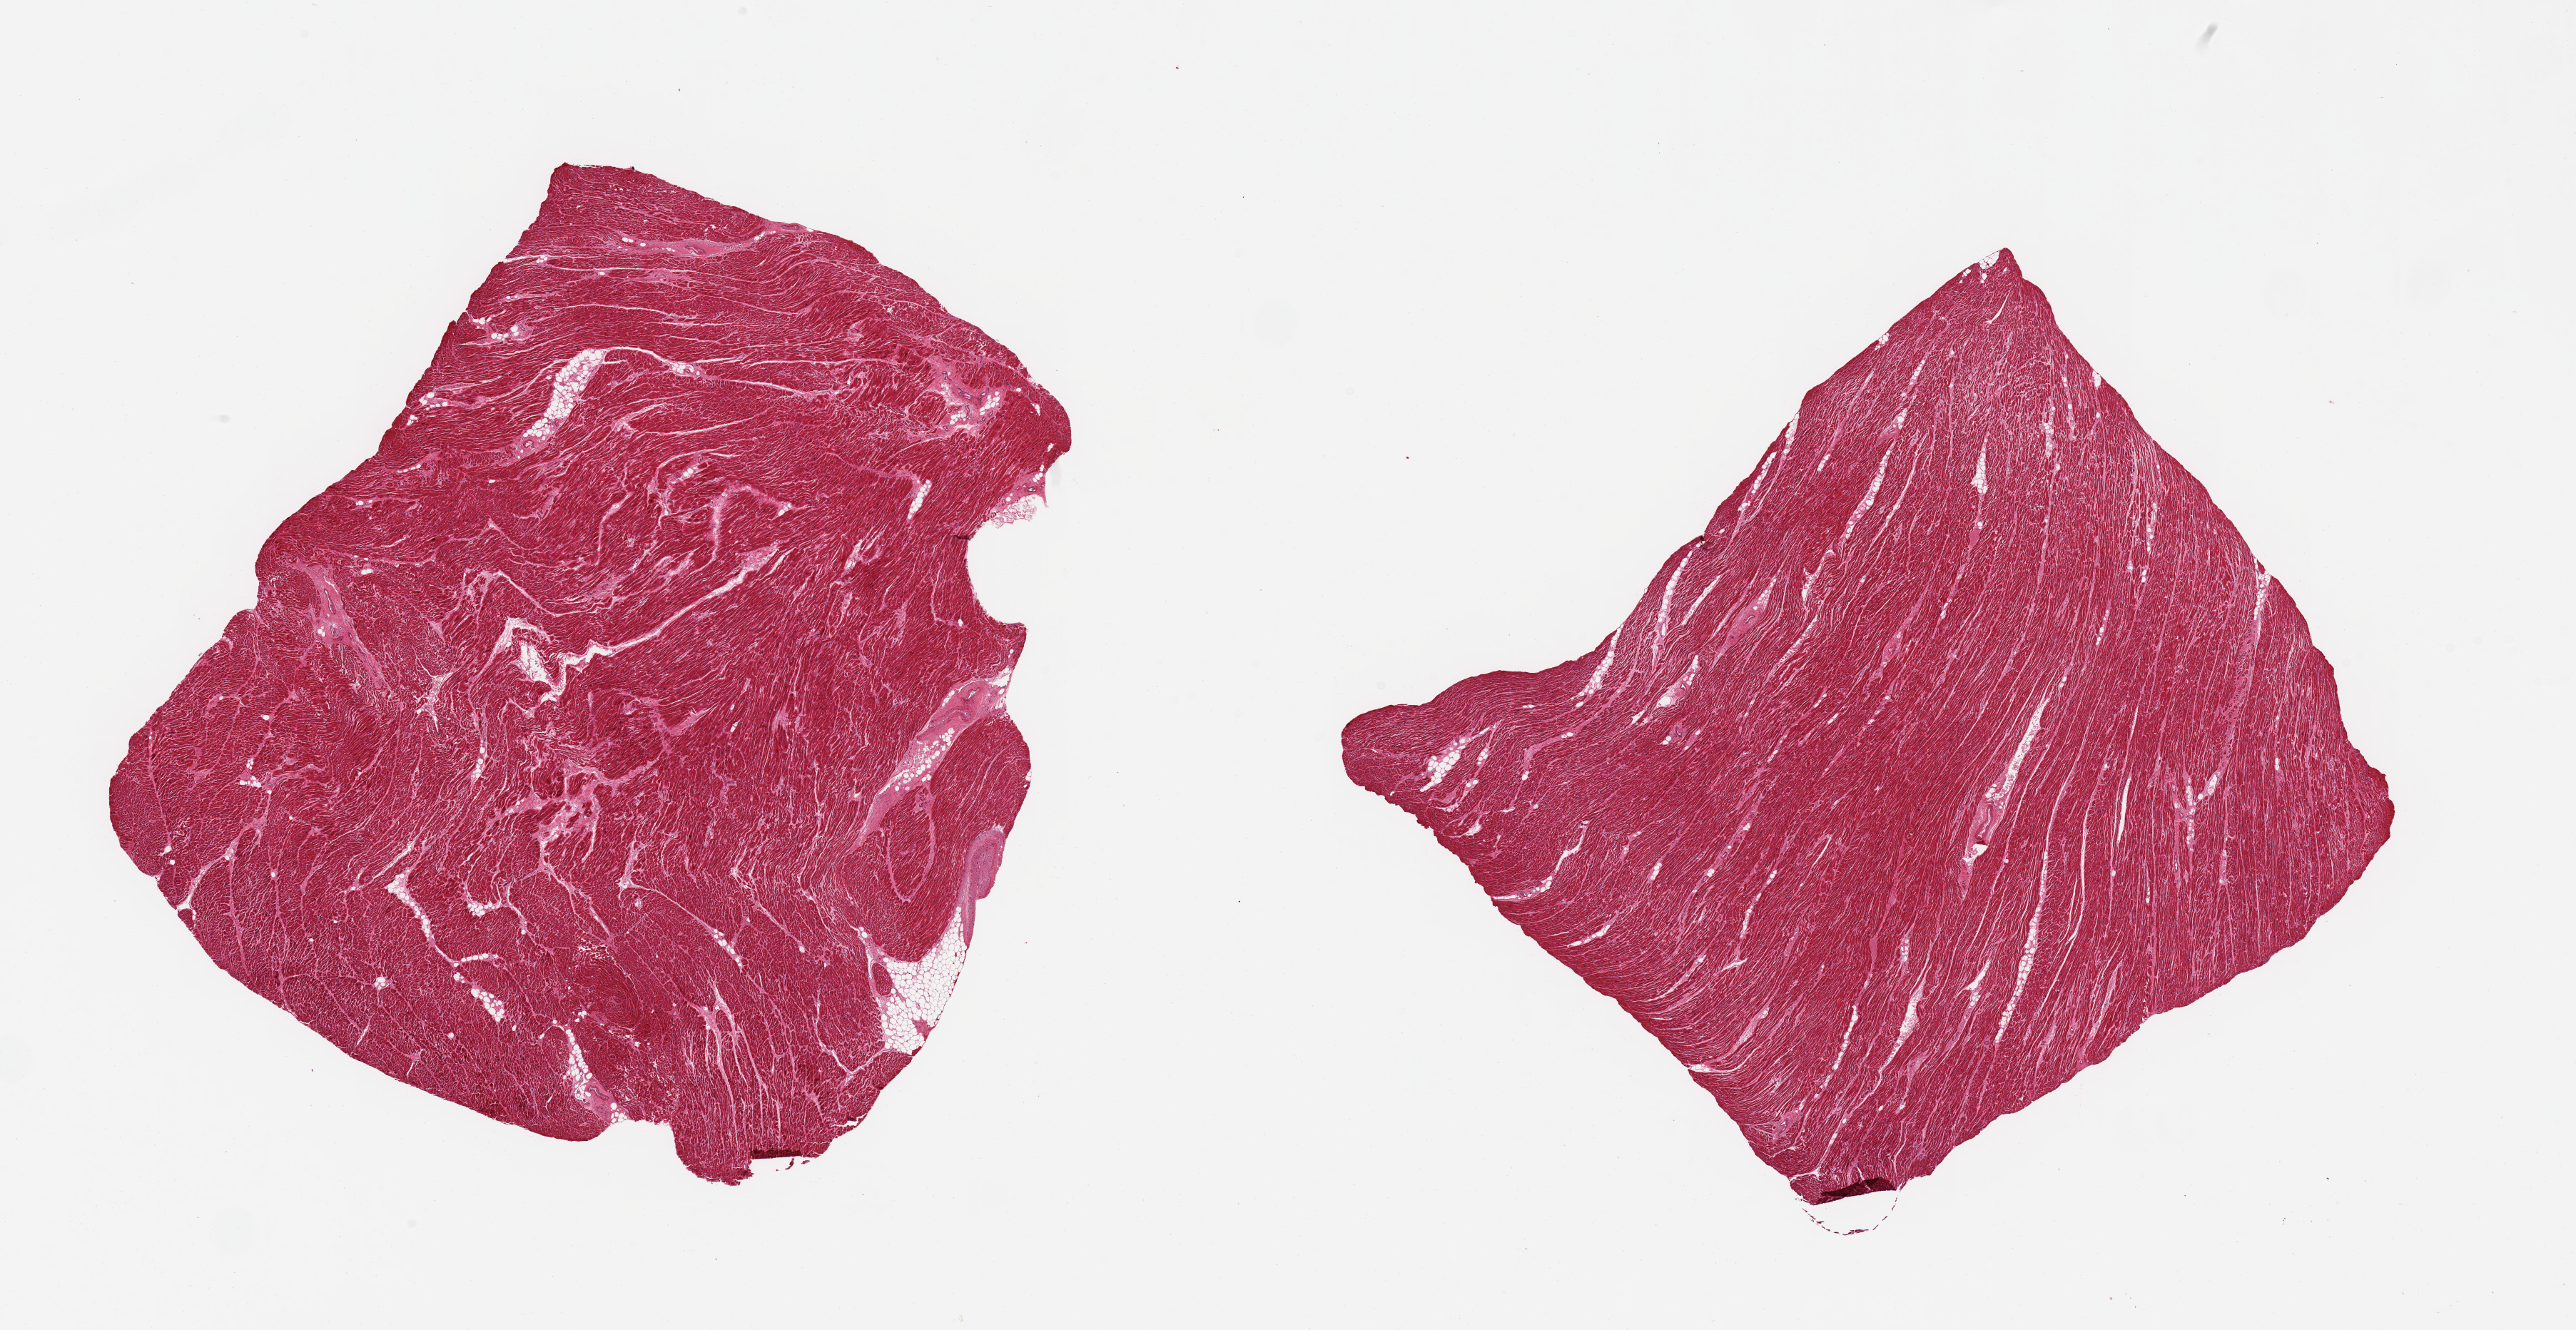
Hematoxylin and eosin (H&E) whole-slide image, low-resolution overview of the scanned area, about 28.5 x 14.7 mm, PAXgene-fixed, paraffin-embedded tissue, target tissue: heart, tissue donor sample. Male donor.
Reviewer comment on this tissue sample: 2 pieces; scattered enlarged nuclei; minimal fat content.